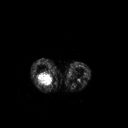
FDG PET of an extremity soft-tissue mass (from a PET/CT study), one axial slice. Position 183 of 267 along the scan axis. 3.27 mm slice thickness. 128 × 128 image matrix. Female patient, age 62 years. Case-level facts recorded for this patient, not image findings: histological type: liposarcoma; site of the primary tumour: right thigh.
Structures marked on this image (expert contour drawn on MRI and transferred to this co-registered scan by the dataset authors):
- gross tumour volume (mass): bounding box (x1, y1, x2, y2) in pixels: (36, 72, 53, 86)